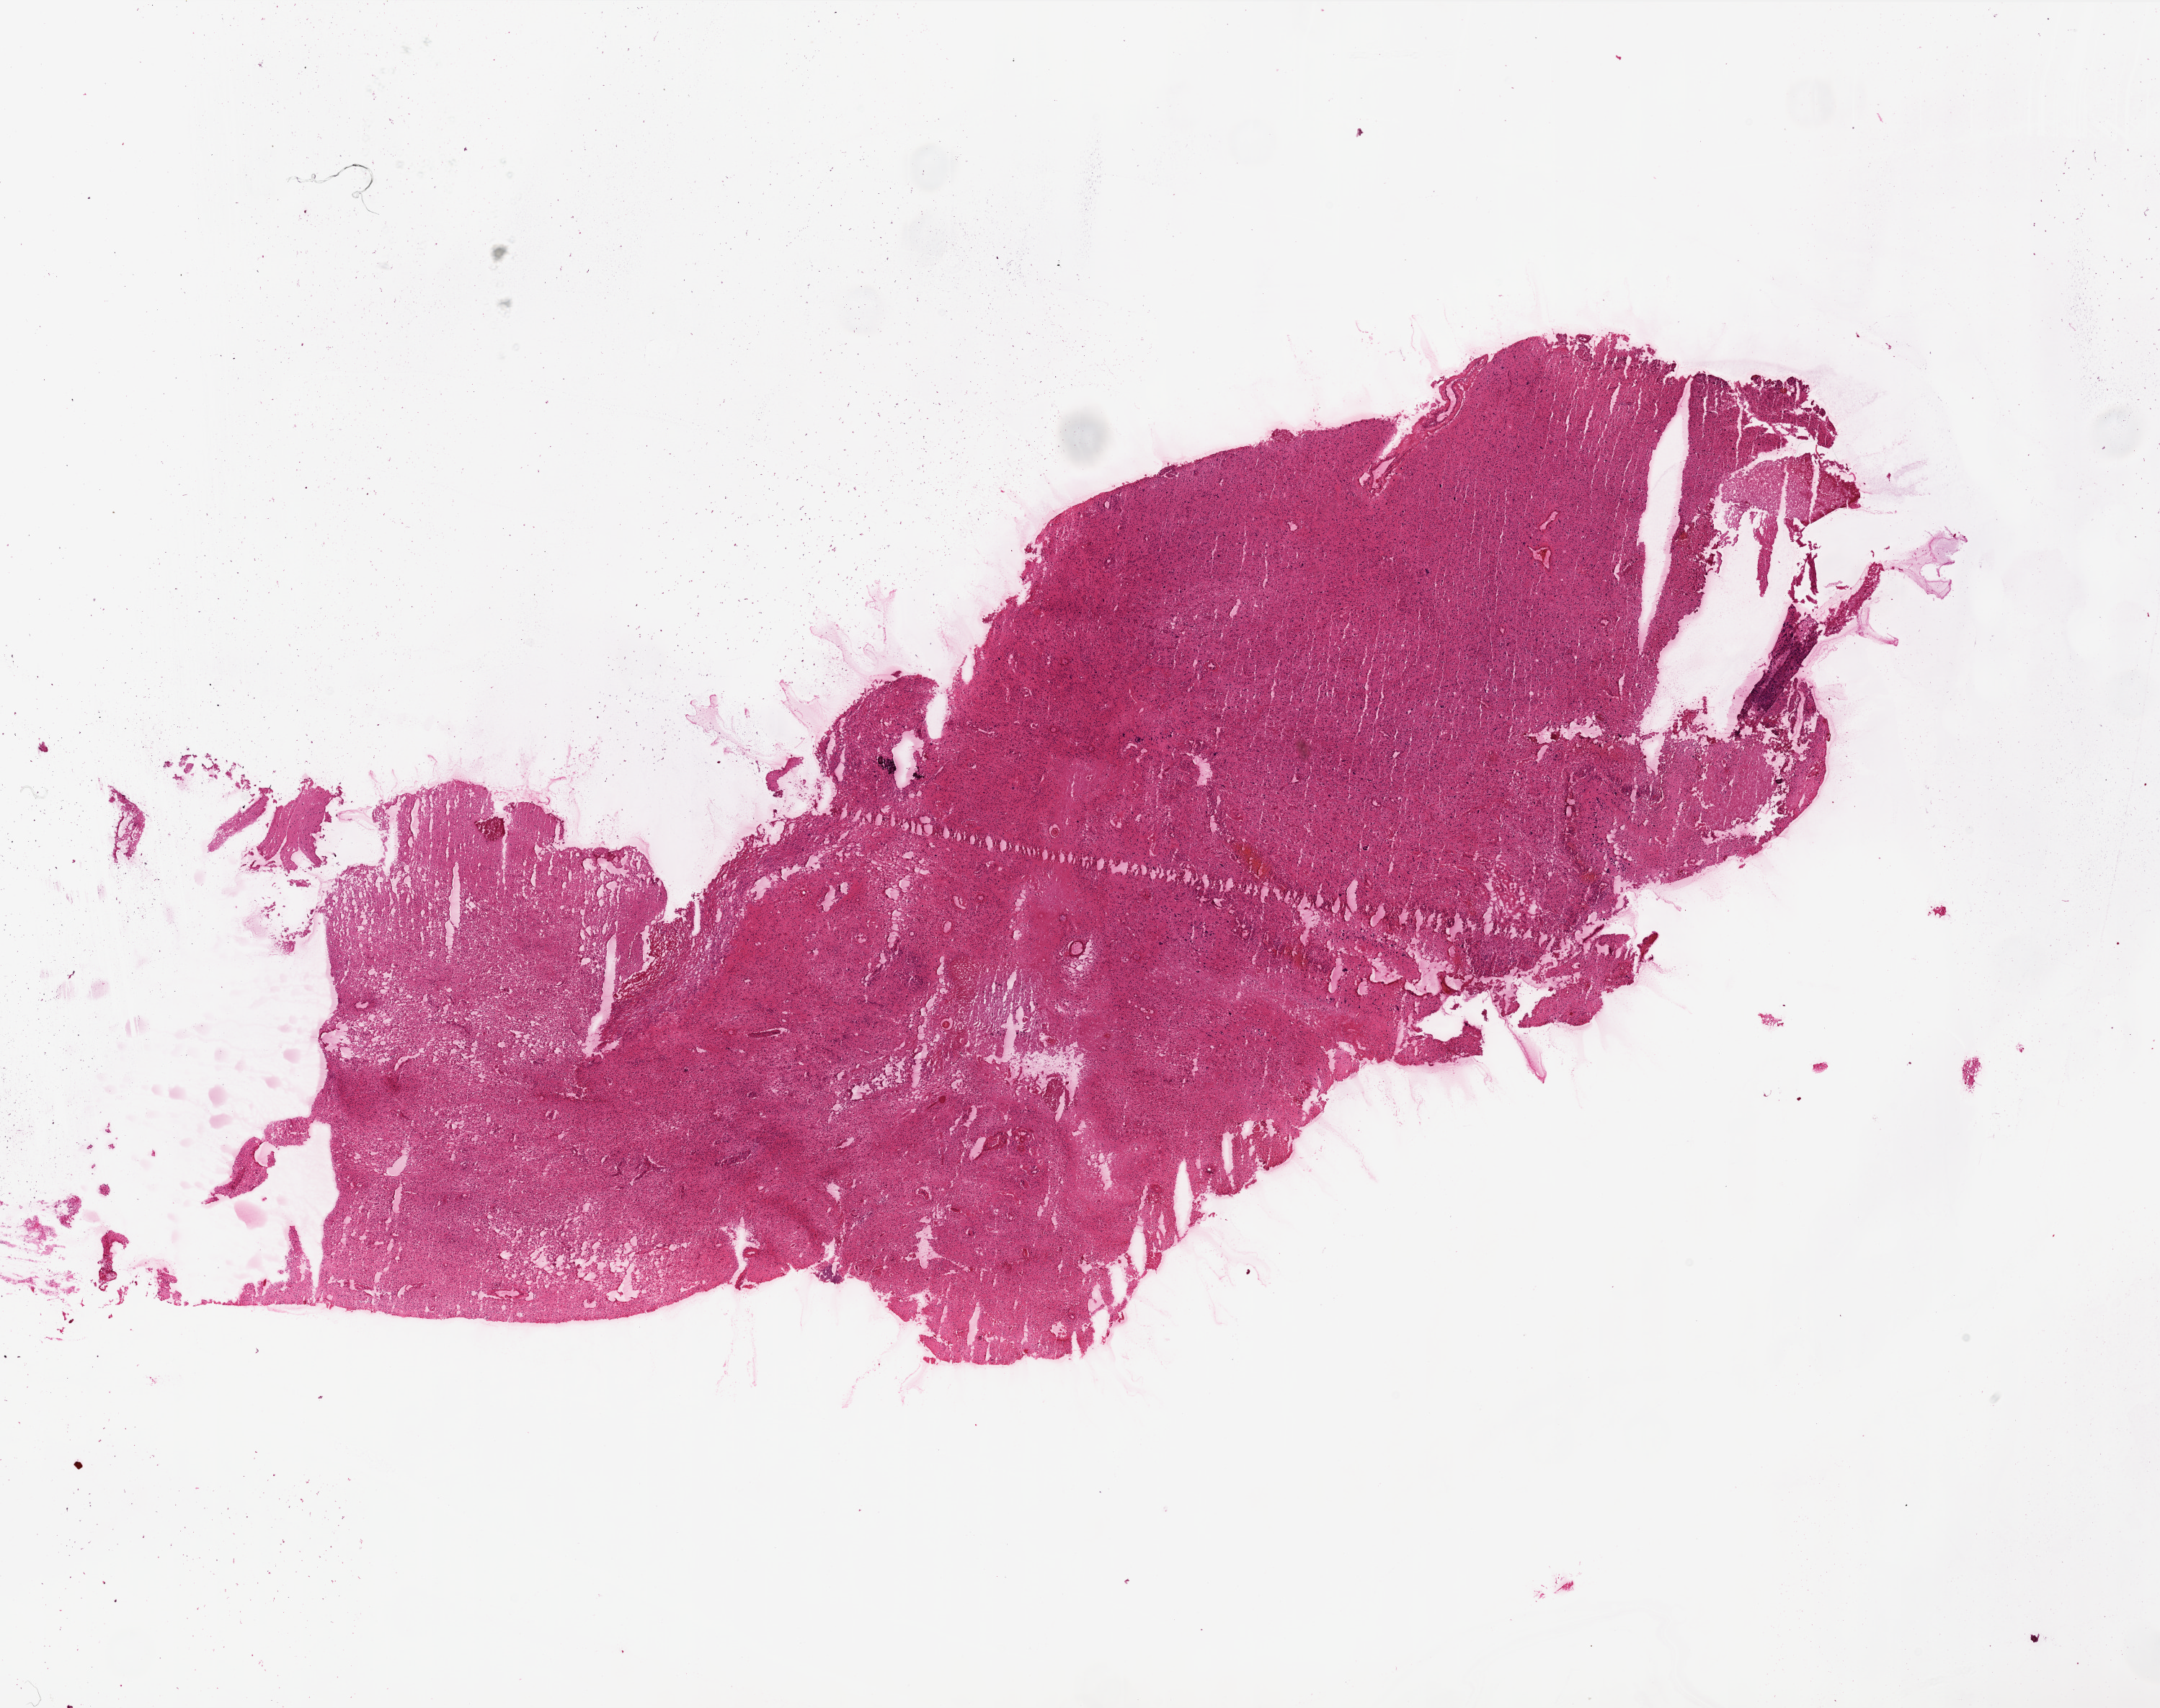
Whole-slide histology image, Hematoxylin and eosin (H&E) stained — whole scanned area (about 24.1 x 19.1 mm) shown as a low-resolution overview; frozen section from the top of the tissue portion; primary tumour sample from the brain. Female, age 66 years at initial diagnosis. Pathologist review of this section (percent, as recorded): tumour cells 80%, tumour nuclei 100%, normal cells 0%, stromal cells 0%, necrosis 20%.
Diagnosis: Glioblastoma.